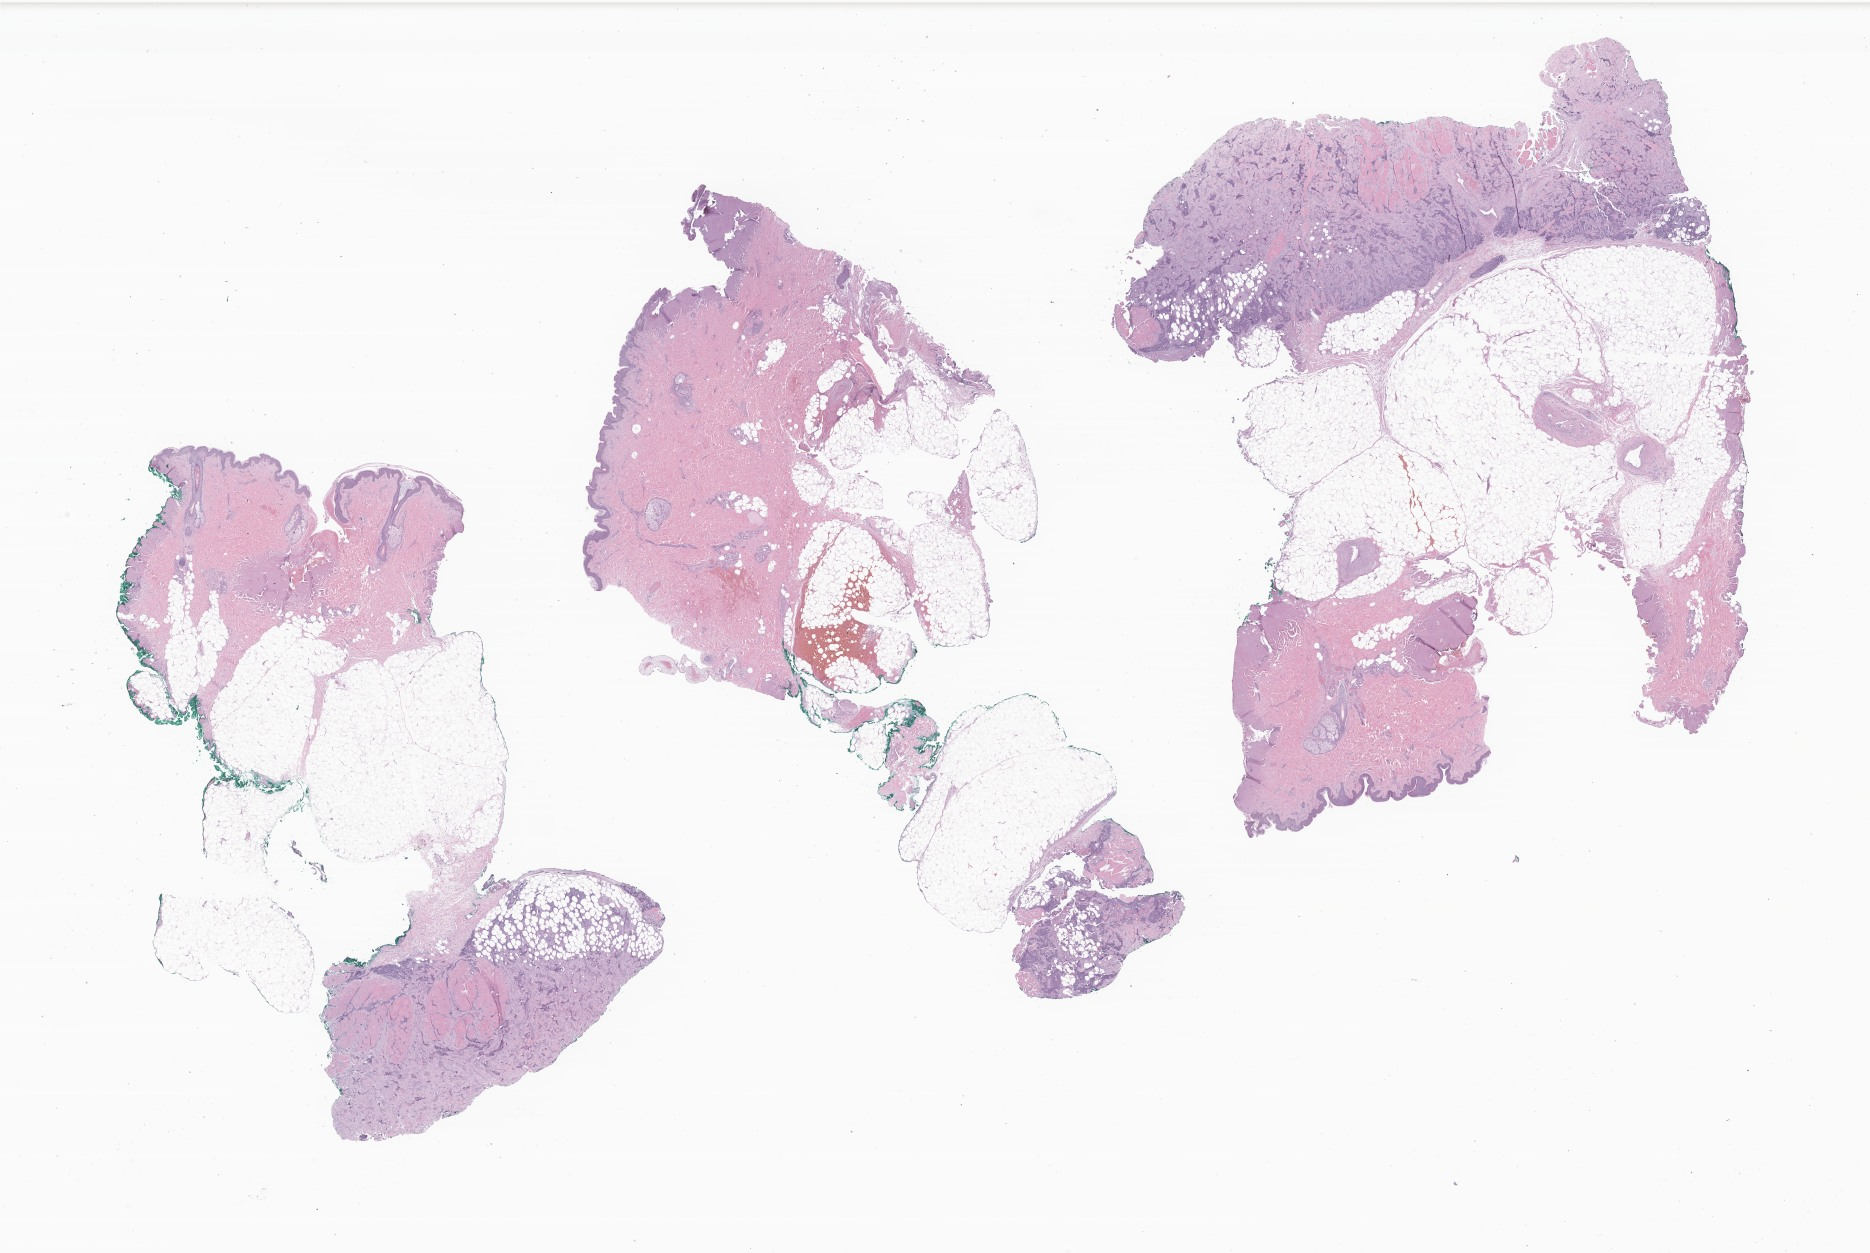
Whole-slide image, hematoxylin and eosin (H&E) stain of tumor tissue from the lung — shown as a low-resolution overview of the whole scanned area (about 31.5 x 21.1 mm), formalin-fixed paraffin-embedded section. Patient male; age 159 months (13 years 3 months).
* diagnosis: Sarcoma, NOS